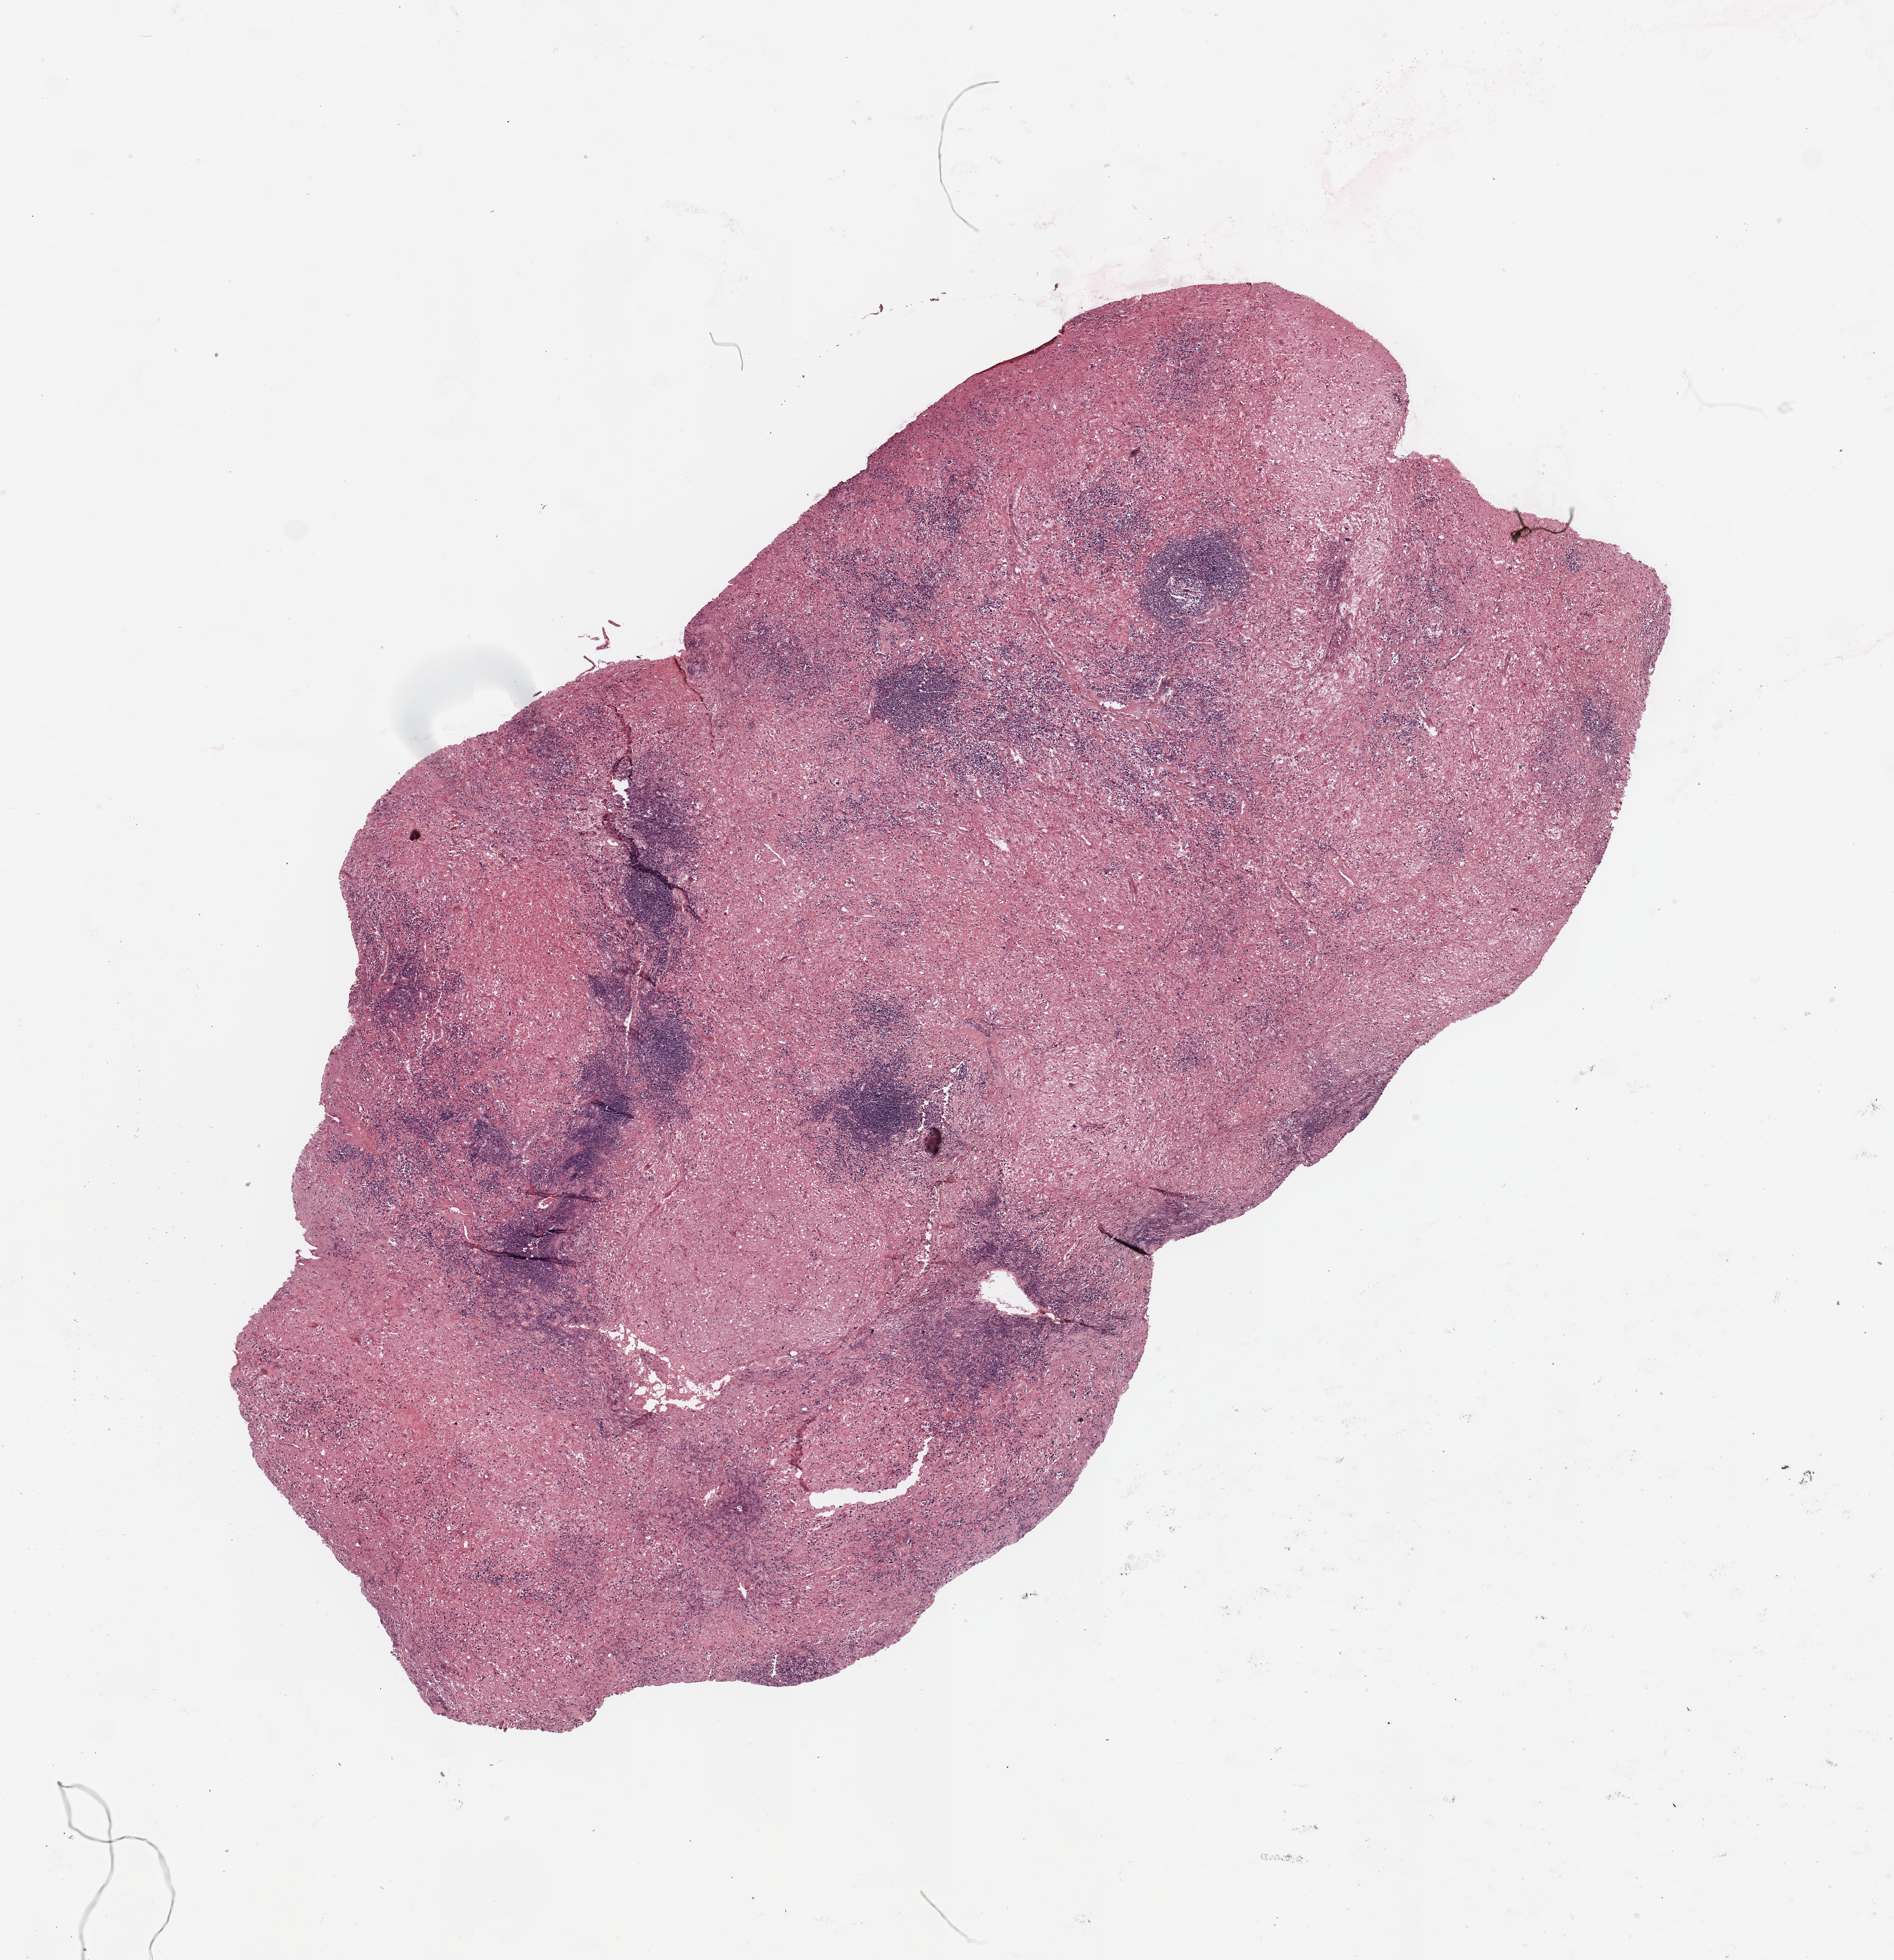
H&E-stained whole-slide image — shown as a low-resolution overview of the whole scanned area (about 11.8 x 12.2 mm). 64-year-old male patient.
Patient diagnosis (cohort enrolment): sarcoma (site not recorded at cohort level).